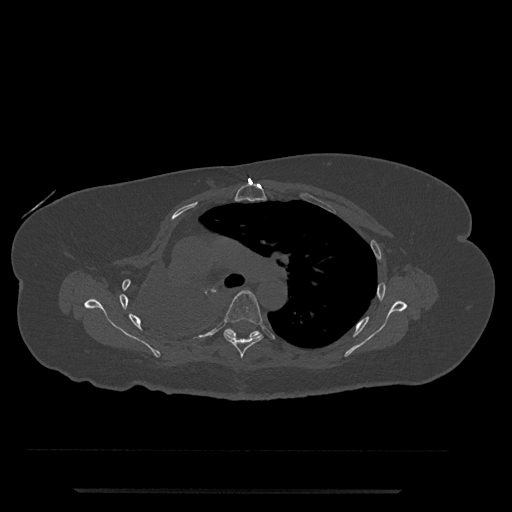
CT including the spine, one axial slice. Reconstruction kernel Br40s/3. 120 kVp. Bone window (W 1800 / L 400 HU). 0.5 mm slice thickness. 512 × 512 image matrix. Patient: female, 51 years. Case-level facts recorded for this patient, not image findings: primary cancer: neuro; vertebrae with lytic lesions (as recorded): T8.
Outlined on this slice (semi-automatically segmented with operator editing):
- T5 vertebra: box from (x=223, y=290) to (x=263, y=358) px
- T6 vertebra: (x=224, y=328)–(x=261, y=339)